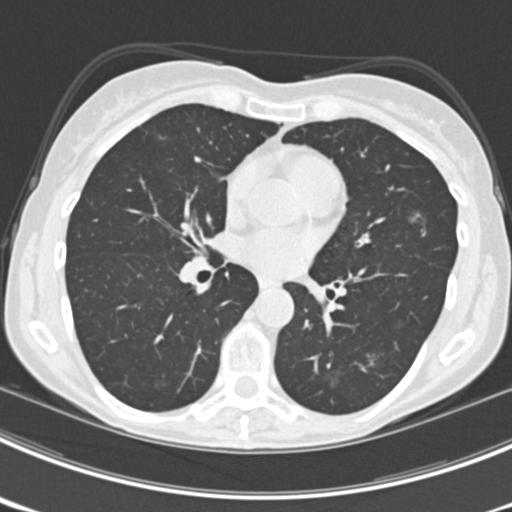
Chest CT (low-dose screening protocol), one axial image, third screening round (two years after baseline), lung window (W 1500 / L -600 HU), 2 mm slice thickness, slice 104 of 225 in the series. Female participant, aged 63 years at enrolment. Current smoker at enrolment.
Expert reader's lesion annotation, bounding box (x1, y1, x2, y2) in pixels: (404, 200, 440, 236). The screening reader recorded 9 non-calcified nodules or masses ≥4 mm on this exam (left upper lobe, right upper lobe, left upper lobe, left lower lobe, right middle lobe, left lower lobe, left lower lobe, right lower lobe, right lower lobe); which of them this box marks is not recorded. Participant outcome: lung cancer diagnosed 15 days after this screen — bronchiolo-alveolar adenocarcinoma, NOS, right upper lobe, right middle lobe, right lower lobe, left upper lobe, left lower lobe, moderately differentiated (G2), stage IV (AJCC 6th edition).